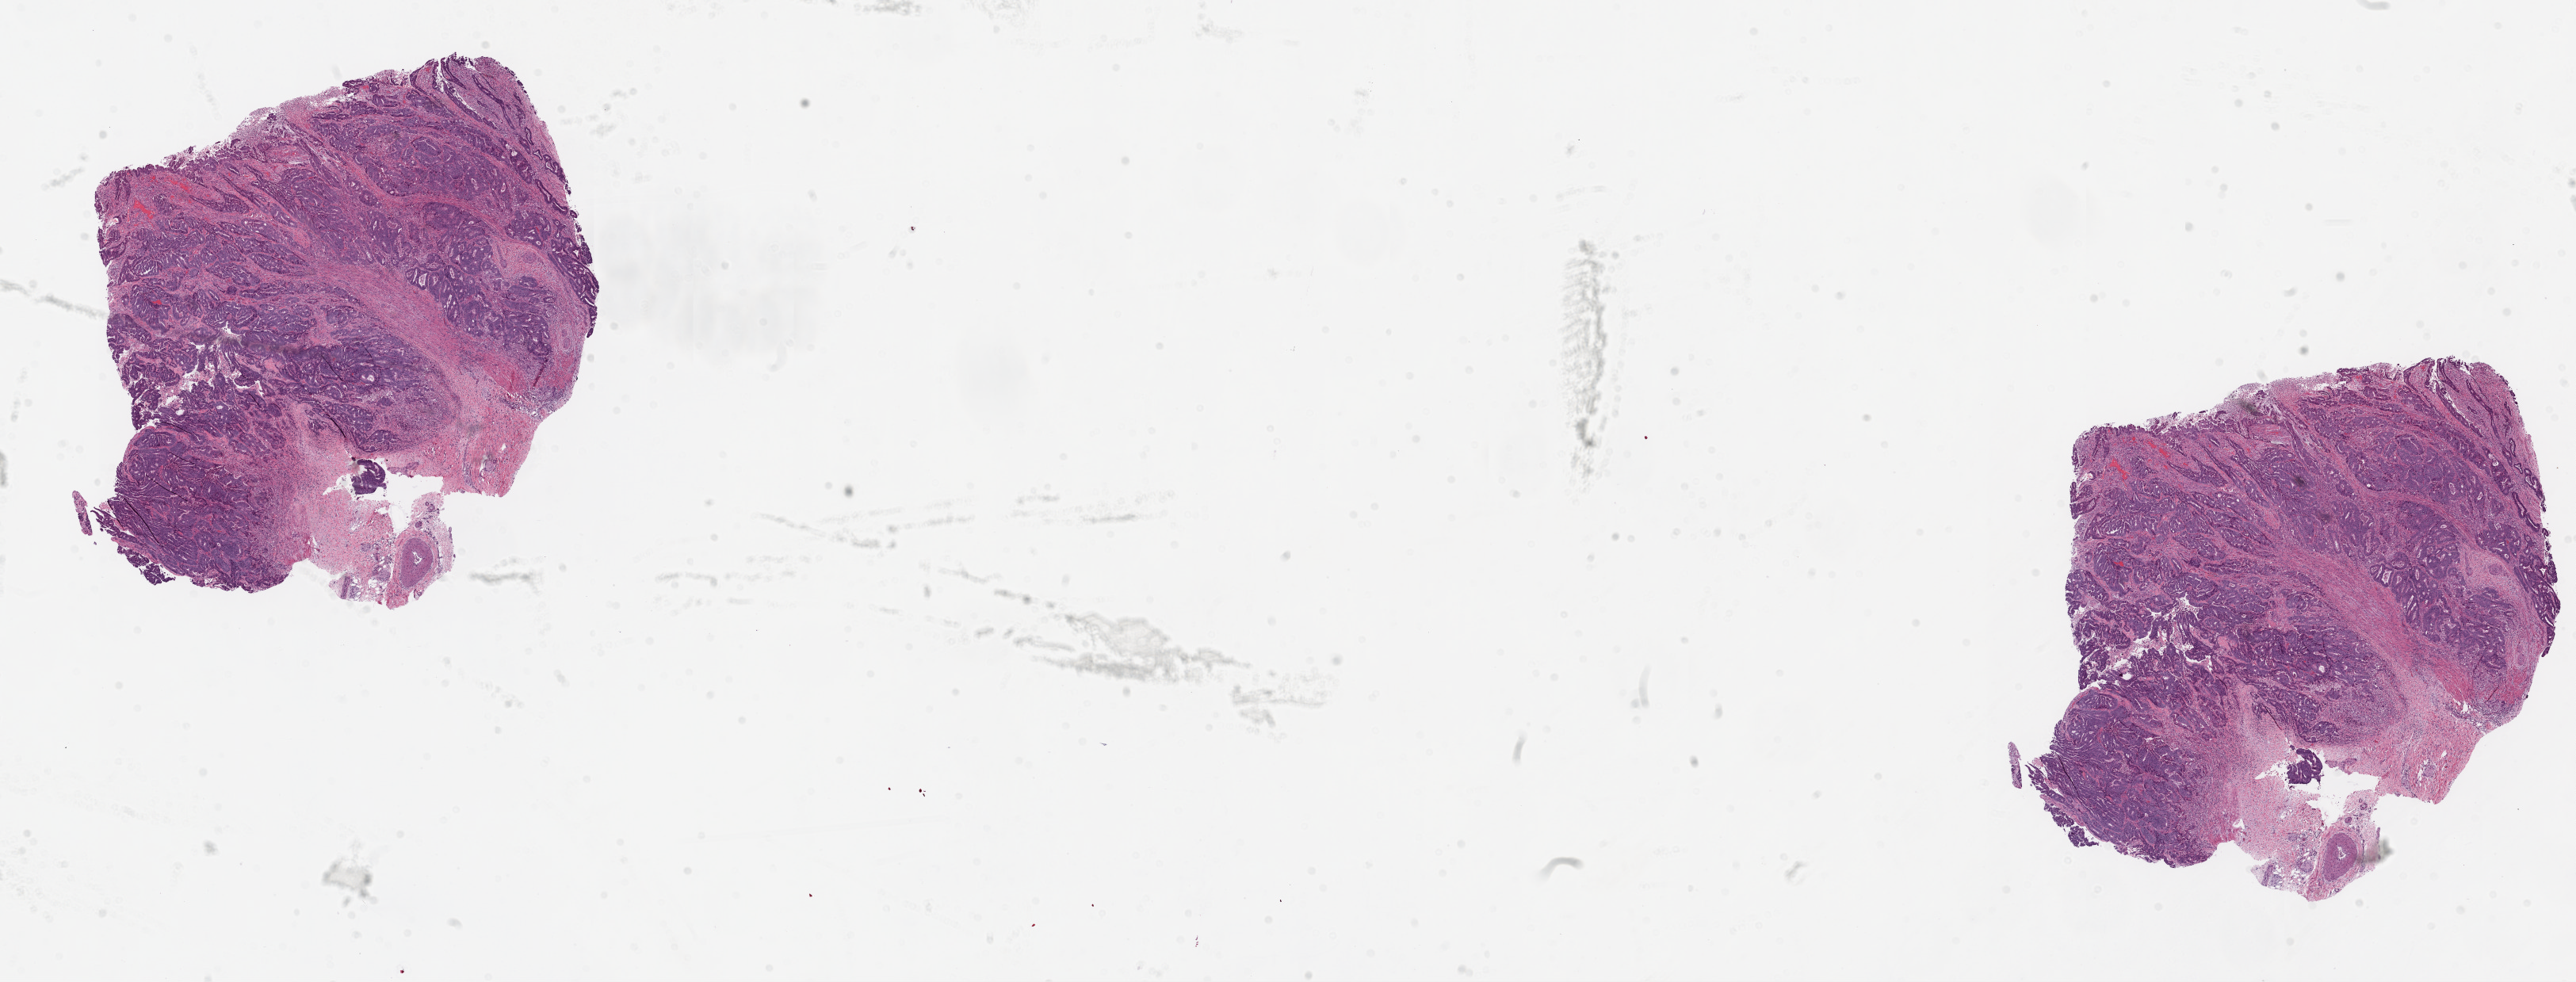
Digitized H&E-stained tissue section (whole slide), whole scanned area (about 26.1 x 9.9 mm, from a 20x scan) shown as a low-resolution overview. Frozen section from the top of the tissue portion. Colon, primary tumour sample. Male patient; age at initial diagnosis 85 years. Composition of this section per pathologist review: tumour cells 75%, tumour nuclei 70%, normal cells 5%, stromal cells 15%, necrosis 5%.
- pathologic diagnosis: Adenocarcinoma, NOS (sigmoid colon)
- AJCC pathologic stage: IV (6th edition)